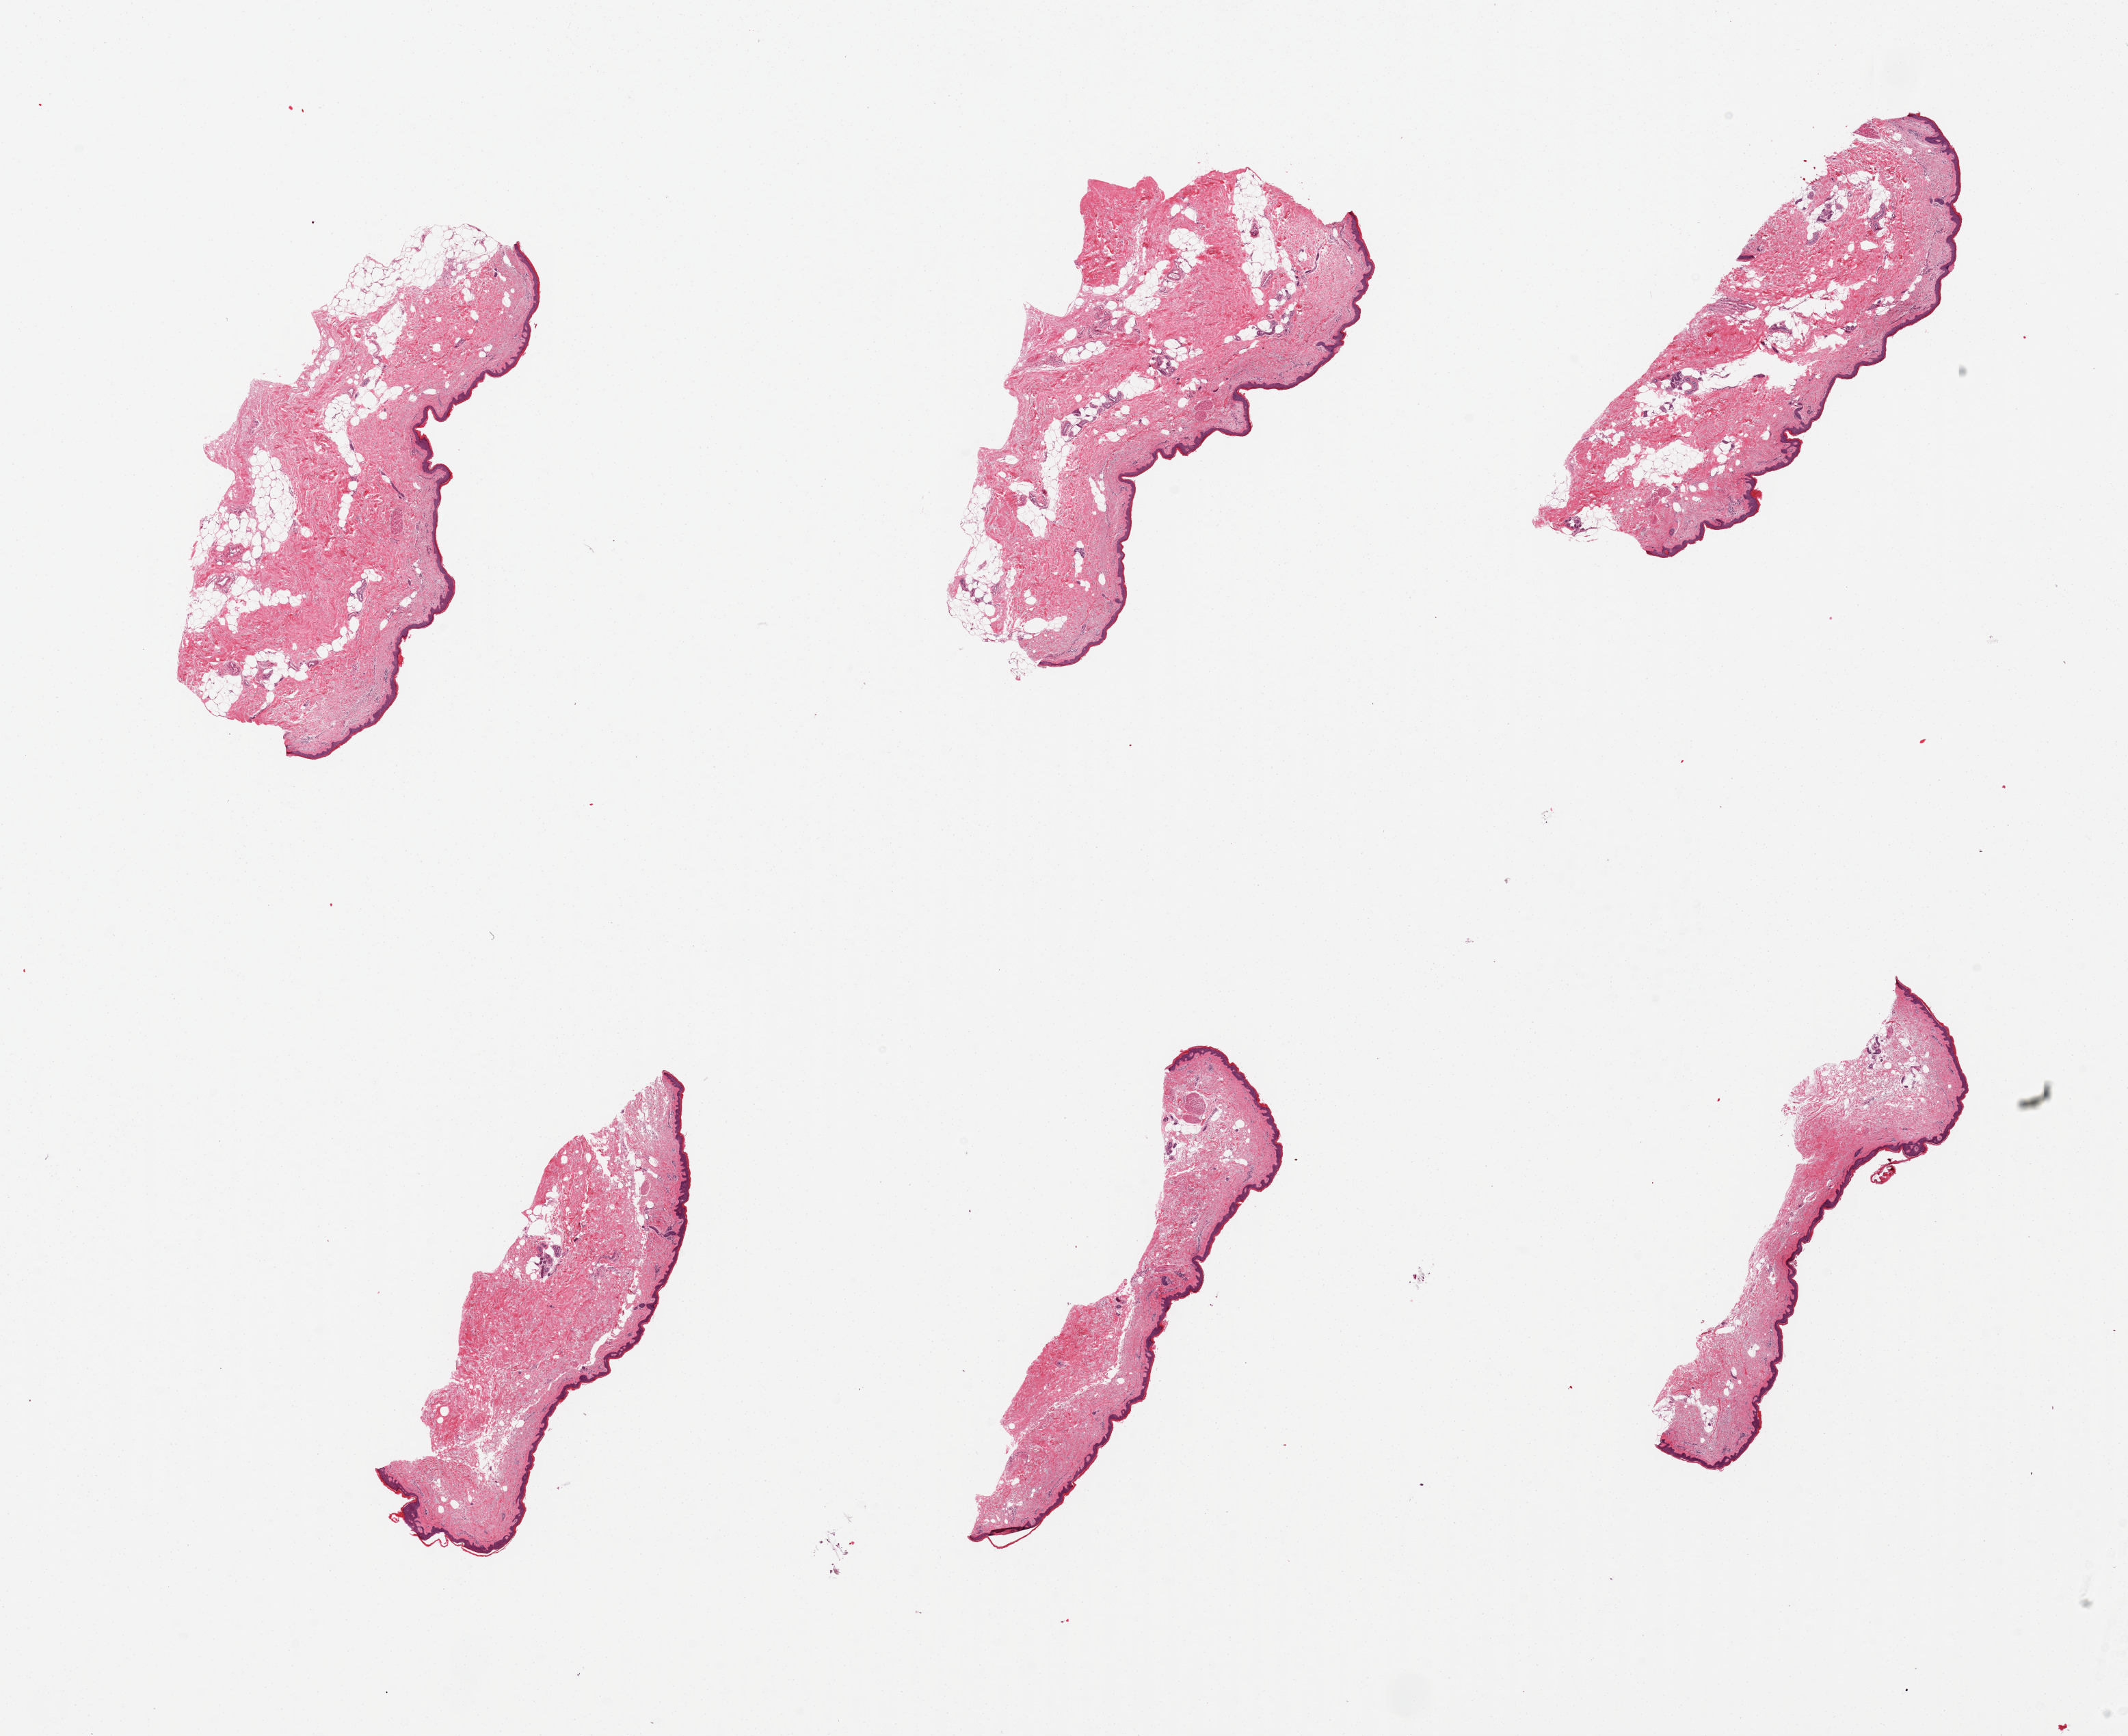
Whole-slide image, H&E stain, low-resolution overview of the scanned area, about 24.6 x 20.1 mm (acquisition: 20x scan), PAXgene-fixed, paraffin-embedded tissue, target tissue: skin of lower leg, donor tissue sample. Donor sex: female.
- review note (as recorded): 6 pieces, minimal fat, squamous epithelium is ~50-70 microns